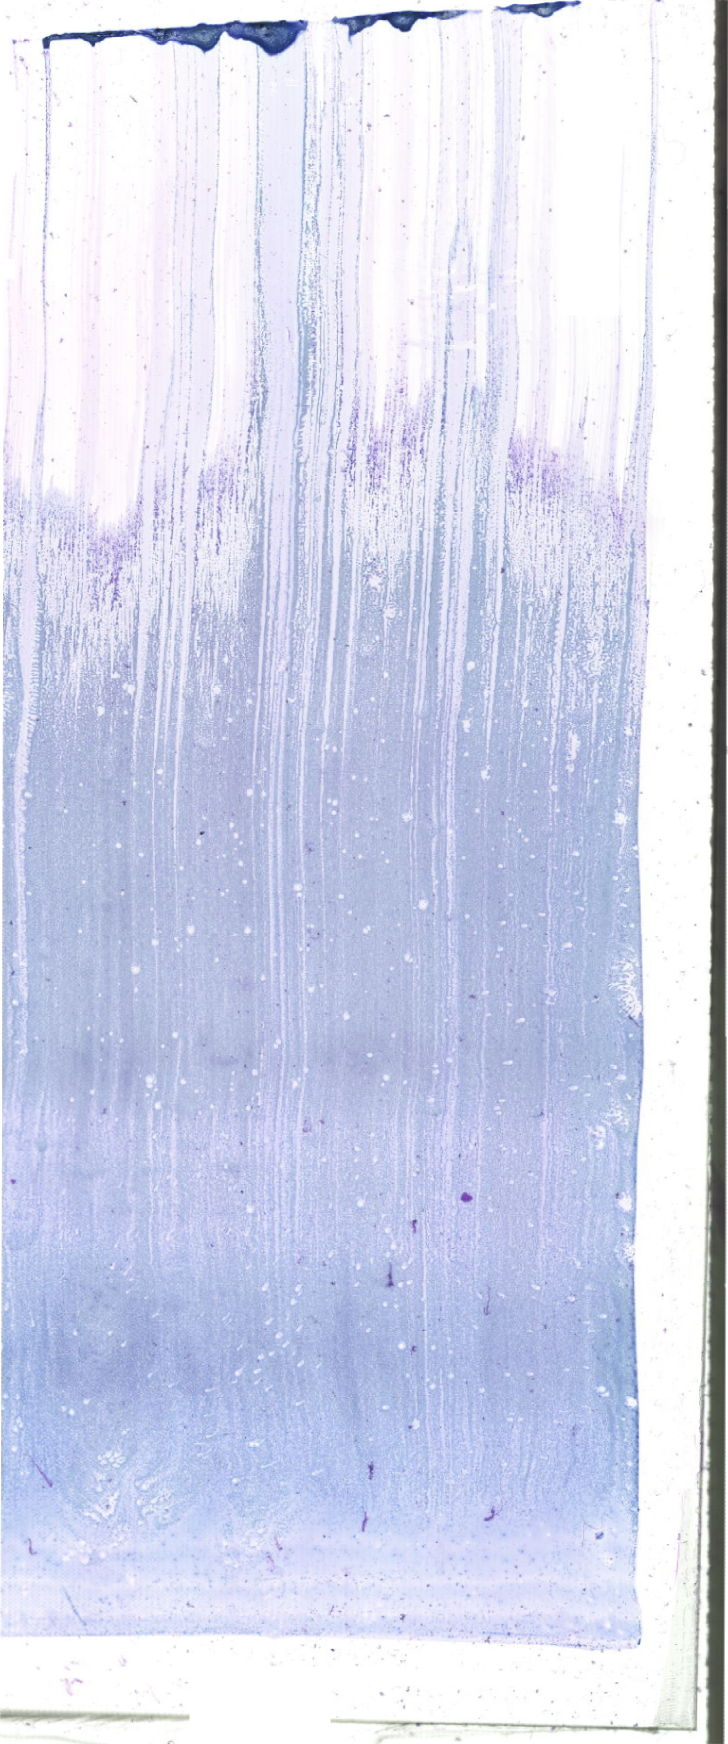
May-Grünwald-Giemsa (MGG)-stained marrow aspirate smear (whole slide), shown as a low-resolution overview of the whole scanned area (about 20.6 x 49.4 mm). Male patient.
Diagnosis: Acute Myeloid Leukemia without Maturation.